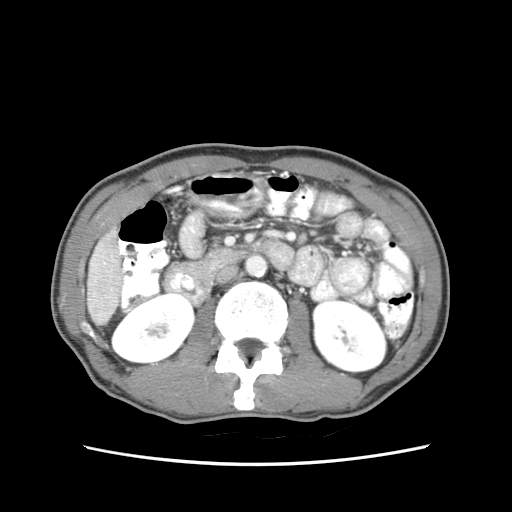
Contrast-enhanced abdominal CT (liver protocol), one axial slice; position 15 of 79 along the scan axis; 120 kVp; soft-tissue window (W 400 / L 40 HU); 2.5 mm slice thickness; 512 × 512 image matrix. Case-level facts recorded for this patient, not image findings: diagnosis: hepatocellular carcinoma (patient treated with transarterial chemoembolisation; whether this scan precedes or follows treatment is not stated here); TNM stage (as recorded): Stage-IIIB; Child-Pugh class: A; tumour differentiation: moderately differentiated.
Outlined on this slice (semi-automatically segmented with operator editing):
- liver parenchyma outside the tumour (the mass and vessels are separate outlines, so this box may not span the whole liver): bounding box [x1, y1, x2, y2] px = [88, 228, 122, 322]
- liver vessels: [110, 245, 120, 273]